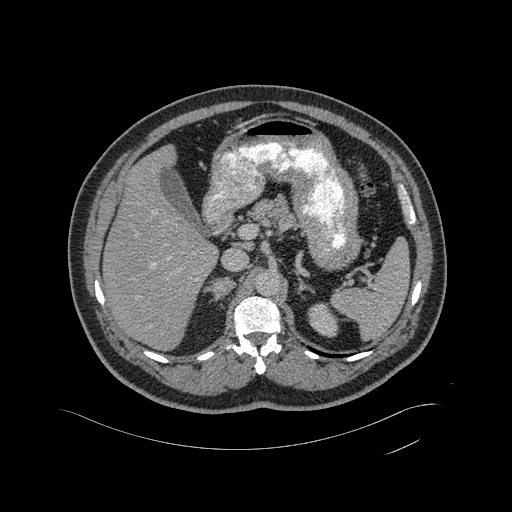
Contrast-enhanced abdominal CT, one axial slice. Slice 316 of 433 in the series (ordered by position). 120 kVp. Soft-tissue window (W 400 / L 40 HU). 2 mm slice thickness. 512 × 512 image matrix, field of view 500 × 500 mm. Male patient, age 56 years. Case-level facts recorded for this patient, not image findings: diagnosis: adrenocortical carcinoma; tumour side: right adrenal; tumour size at pathology: 11.6 cm; Ki-67 index: 50 %; stage (as recorded): 3.
Outlined on this slice (semi-automatically segmented with operator editing):
- mass: box from (x=212, y=280) to (x=232, y=294) px